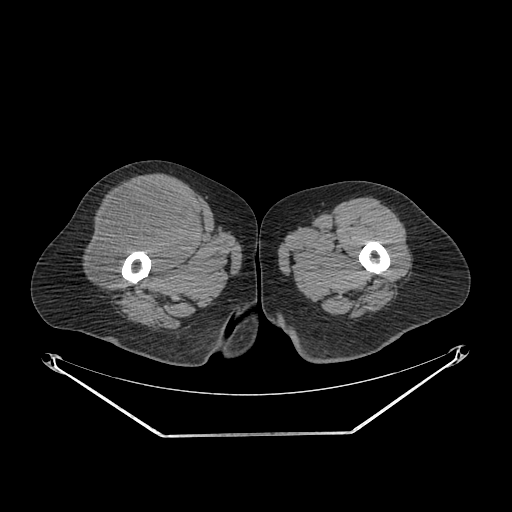
CT of an extremity soft-tissue mass (from a PET/CT study), one axial slice. Position 261 of 311 along the scan axis. 140 kVp. Soft-tissue window (W 400 / L 40 HU). 3.75 mm slice thickness. 512 × 512 image matrix, field of view 500 × 500 mm. Female patient. Case-level facts recorded for this patient, not image findings: histological type: pleiomorphic undifferentiated sarcoma; grade: high; site of the primary tumour: right quadricep.
Structures marked on this image (expert contour drawn on MRI and transferred to this co-registered scan by the dataset authors):
- tumour plus oedema (research contour): box from (x=91, y=185) to (x=195, y=284) px
- tumour (research contour): (x=91, y=185)–(x=195, y=284)